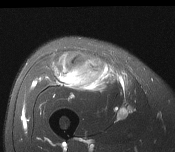
MRI of an extremity soft-tissue mass, one axial slice; position 71 of 116 along the scan axis; T2-weighted fat-saturated; MR volume resampled by the dataset authors to the PET/CT grid (not the native acquisition matrix); 3.27 mm slice thickness; 175 × 152 image matrix, field of view 171 × 148 mm. Male patient. Case-level facts recorded for this patient, not image findings: histological type: pleiomorphic leiomyosarcoma; grade: intermediate; site of the primary tumour: right thigh.
Annotated regions visible in this slice (expert contour drawn on MRI and transferred to this co-registered scan by the dataset authors):
- gross tumour volume including surrounding oedema: box from (x=54, y=52) to (x=109, y=91) px
- gross tumour volume (mass): (x=65, y=60)–(x=105, y=87)